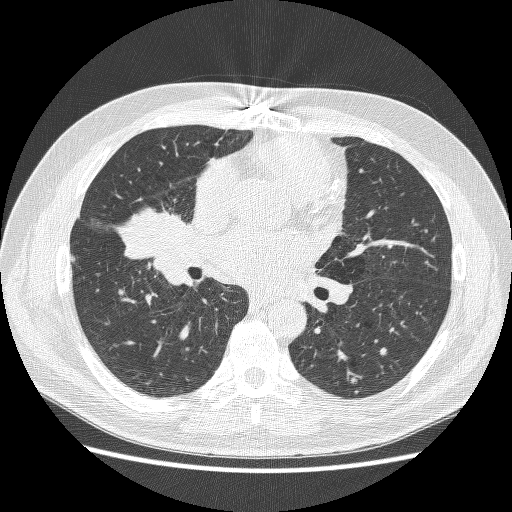
Low-dose screening chest CT, axial slice. Baseline annual screen. Lung window (W 1500 / L -600 HU). Slice 140 of 251 in the series. 512 × 512 image matrix, field of view 360 × 360 mm. Male, age 59 years at enrolment. Former smoker at enrolment.
• Expert-annotated lung lesion, bounding box (x1, y1, x2, y2) in pixels: (123, 192, 197, 264).
• No non-calcified nodule or mass ≥4 mm was recorded by the screening reader at this exam.
• Participant outcome: lung cancer diagnosed 24 days after this screen — adenocarcinoma, NOS, right middle lobe, poorly differentiated (G3), stage IV (AJCC 6th edition), 54 mm at pathology.